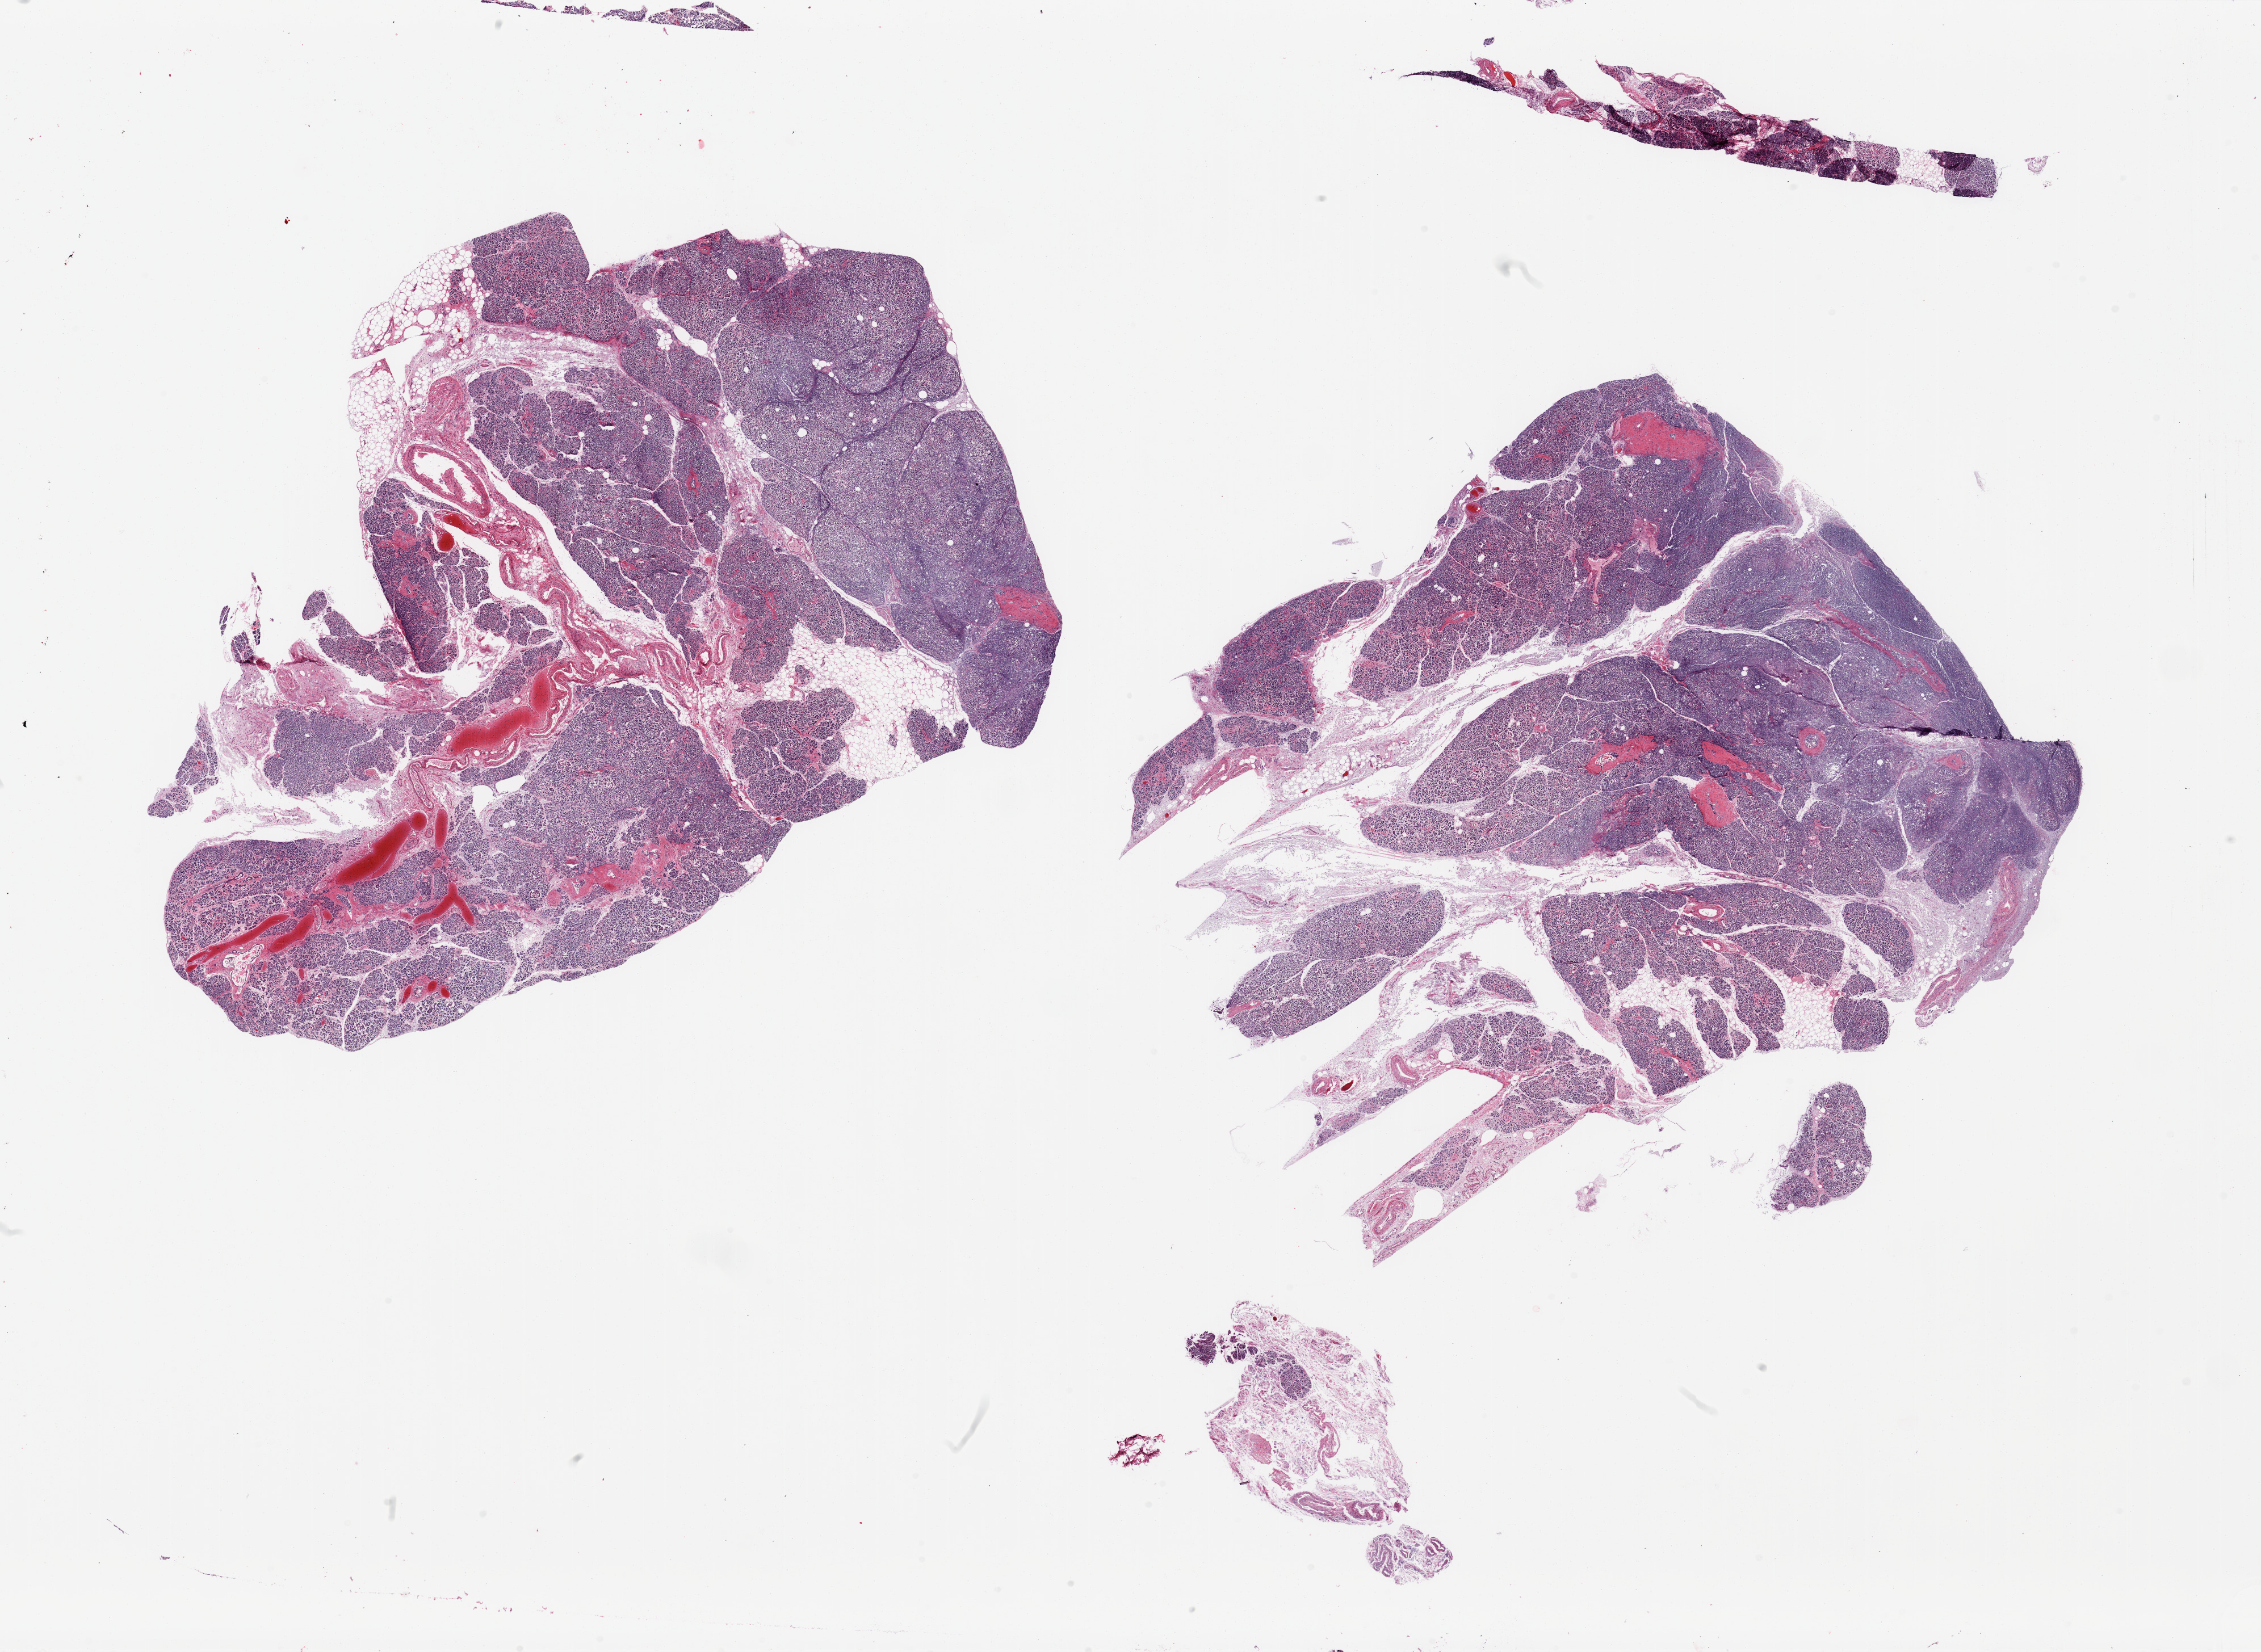
Haematoxylin and eosin whole-slide image — shown as a low-resolution overview of the whole scanned area (about 31.5 x 23.0 mm); PAXgene-fixed, paraffin-embedded tissue; section of pancreas (target tissue); donor tissue sample.
Pathologist's review note for this sample: 2 pieces, advanced saponification; islets not visible.